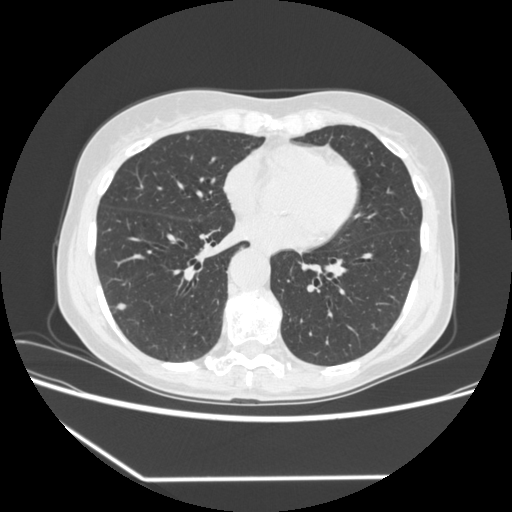
Low-dose screening chest CT, one axial slice. Slice 157 of 323 in the series (ordered by position). 120 kVp. Lung window (W 1500 / L -600 HU). 1.25 mm slice thickness. 512 × 512 image matrix.
Annotated regions visible in this slice (manually delineated by an expert):
- lesion 2 (nodule, lower lobe of right lung): bounding box [x1, y1, x2, y2] px = [118, 303, 126, 310]